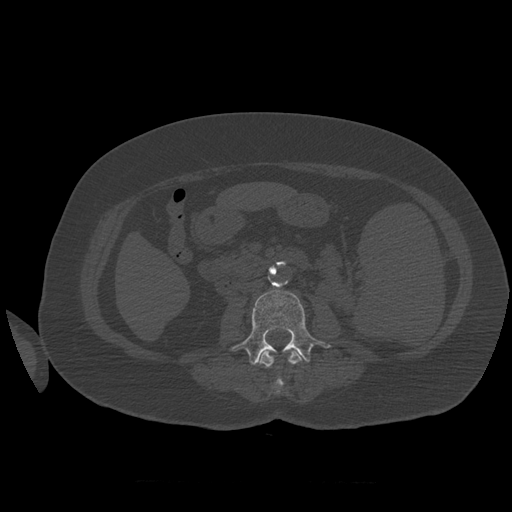
CT including the spine, one axial slice; position 235 of 399 along the scan axis; reconstruction kernel STANDARD; bone window (W 1800 / L 400 HU); 1.25 mm slice thickness; 512 × 512 image matrix, field of view 404 × 404 mm. Patient age 81 years. From the clinical record (not read from this slice): primary cancer: renal; vertebrae with lytic lesions (as recorded): L1.
Structures marked on this image (semi-automatically segmented with operator editing):
- L2 vertebra: bounding box <253,350,306,394> (left, top, right, bottom; pixels)
- L3 vertebra: <230,290,331,365>